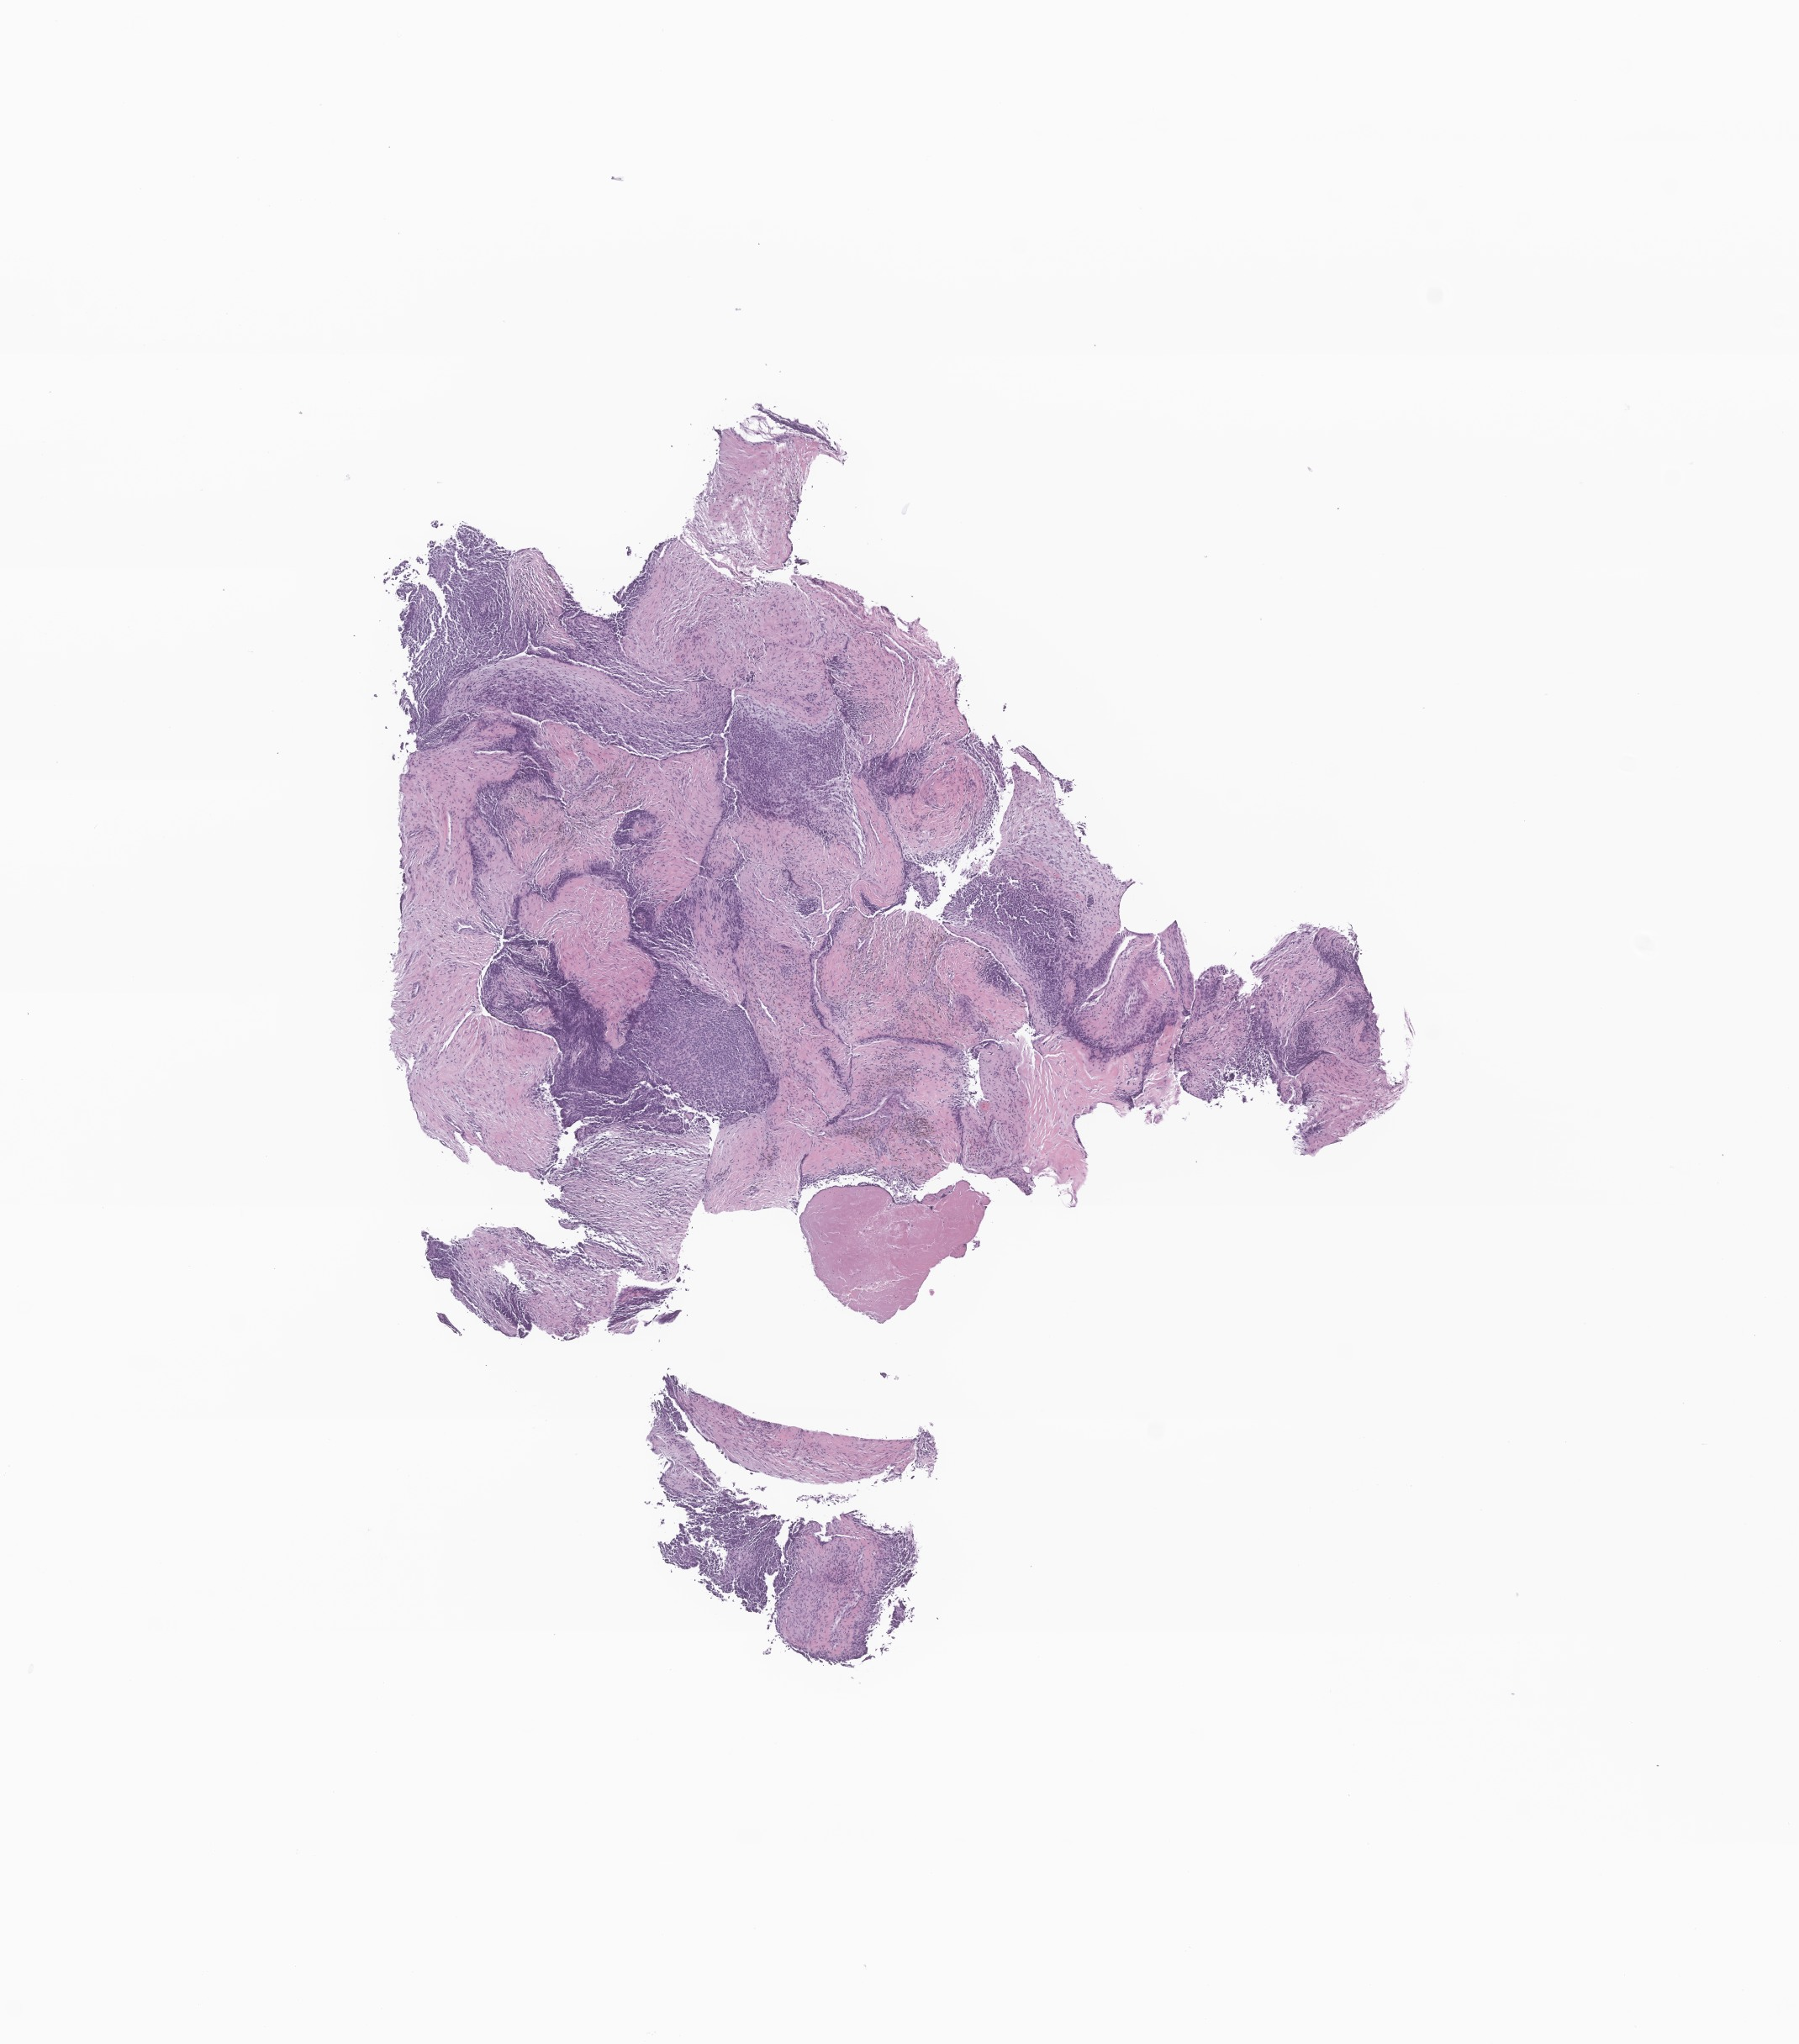
Haematoxylin and eosin whole-slide image of tumor tissue from the soft tissue of pelvis, low-resolution overview of the scanned area, about 9.0 x 10.3 mm. Patient: female, age 168 months (14 years).
Specimen: FFPE section.